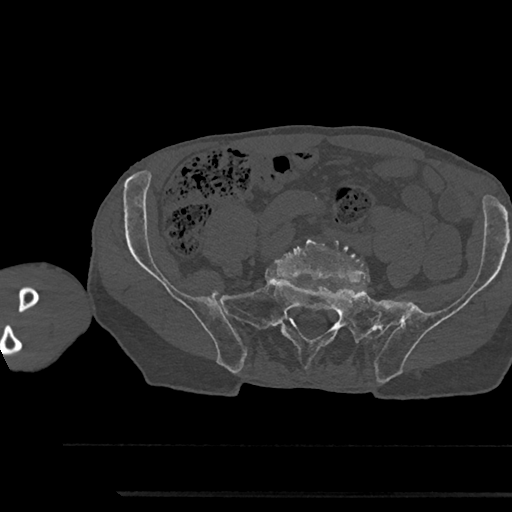
CT including the spine, one axial slice. Slice 307 of 797 in the series (ordered by position). Reconstruction kernel Br40s/3. 120 kVp. Bone window (W 1800 / L 400 HU). 512 × 512 image matrix. Patient: male, 79 years. From the clinical record (not read from this slice): primary cancer: prostate.
Annotated regions visible in this slice (semi-automatic segmentation, software-assisted and operator-edited):
- L5 vertebra: bounding box [x1, y1, x2, y2] px = [275, 234, 369, 285]